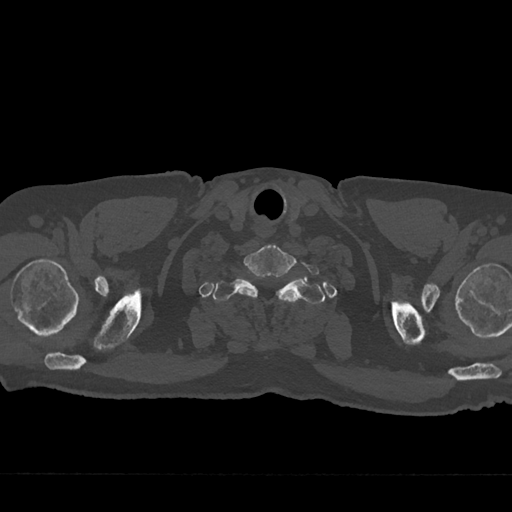
CT including the spine, one axial slice. Position 676 of 797 along the scan axis. 120 kVp. Bone window (W 1800 / L 400 HU). 512 × 512 image matrix, field of view 377 × 377 mm. Male patient, age 75 years. From the clinical record (not read from this slice): primary cancer: renal; vertebrae with lytic lesions (as recorded): T4.
Annotated regions visible in this slice (semi-automatic segmentation, software-assisted and operator-edited):
- T1 vertebra: bounding box <213,272,325,304> (left, top, right, bottom; pixels)